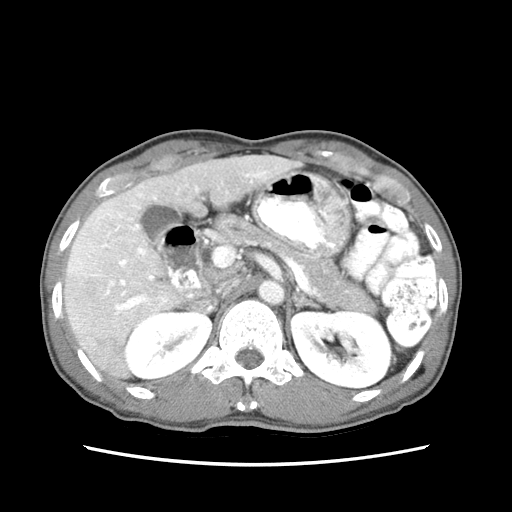
Contrast-enhanced abdominal CT (liver protocol), one axial slice; slice 37 of 79 in the series (ordered by position); soft-tissue window (W 400 / L 40 HU); 2.5 mm slice thickness; 512 × 512 image matrix. Case-level facts recorded for this patient, not image findings: diagnosis: hepatocellular carcinoma (patient treated with transarterial chemoembolisation; whether this scan precedes or follows treatment is not stated here); TNM stage (as recorded): Stage-IIIB; Child-Pugh class: A; tumour differentiation: moderately differentiated; tumour nodularity: multinodular.
Outlined on this slice (semi-automatic segmentation, software-assisted and operator-edited):
- liver parenchyma outside the tumour (the mass and vessels are separate outlines, so this box may not span the whole liver): box from (x=62, y=152) to (x=302, y=382) px
- mass: (x=68, y=249)–(x=102, y=278)
- liver vessels: (x=74, y=164)–(x=285, y=349)